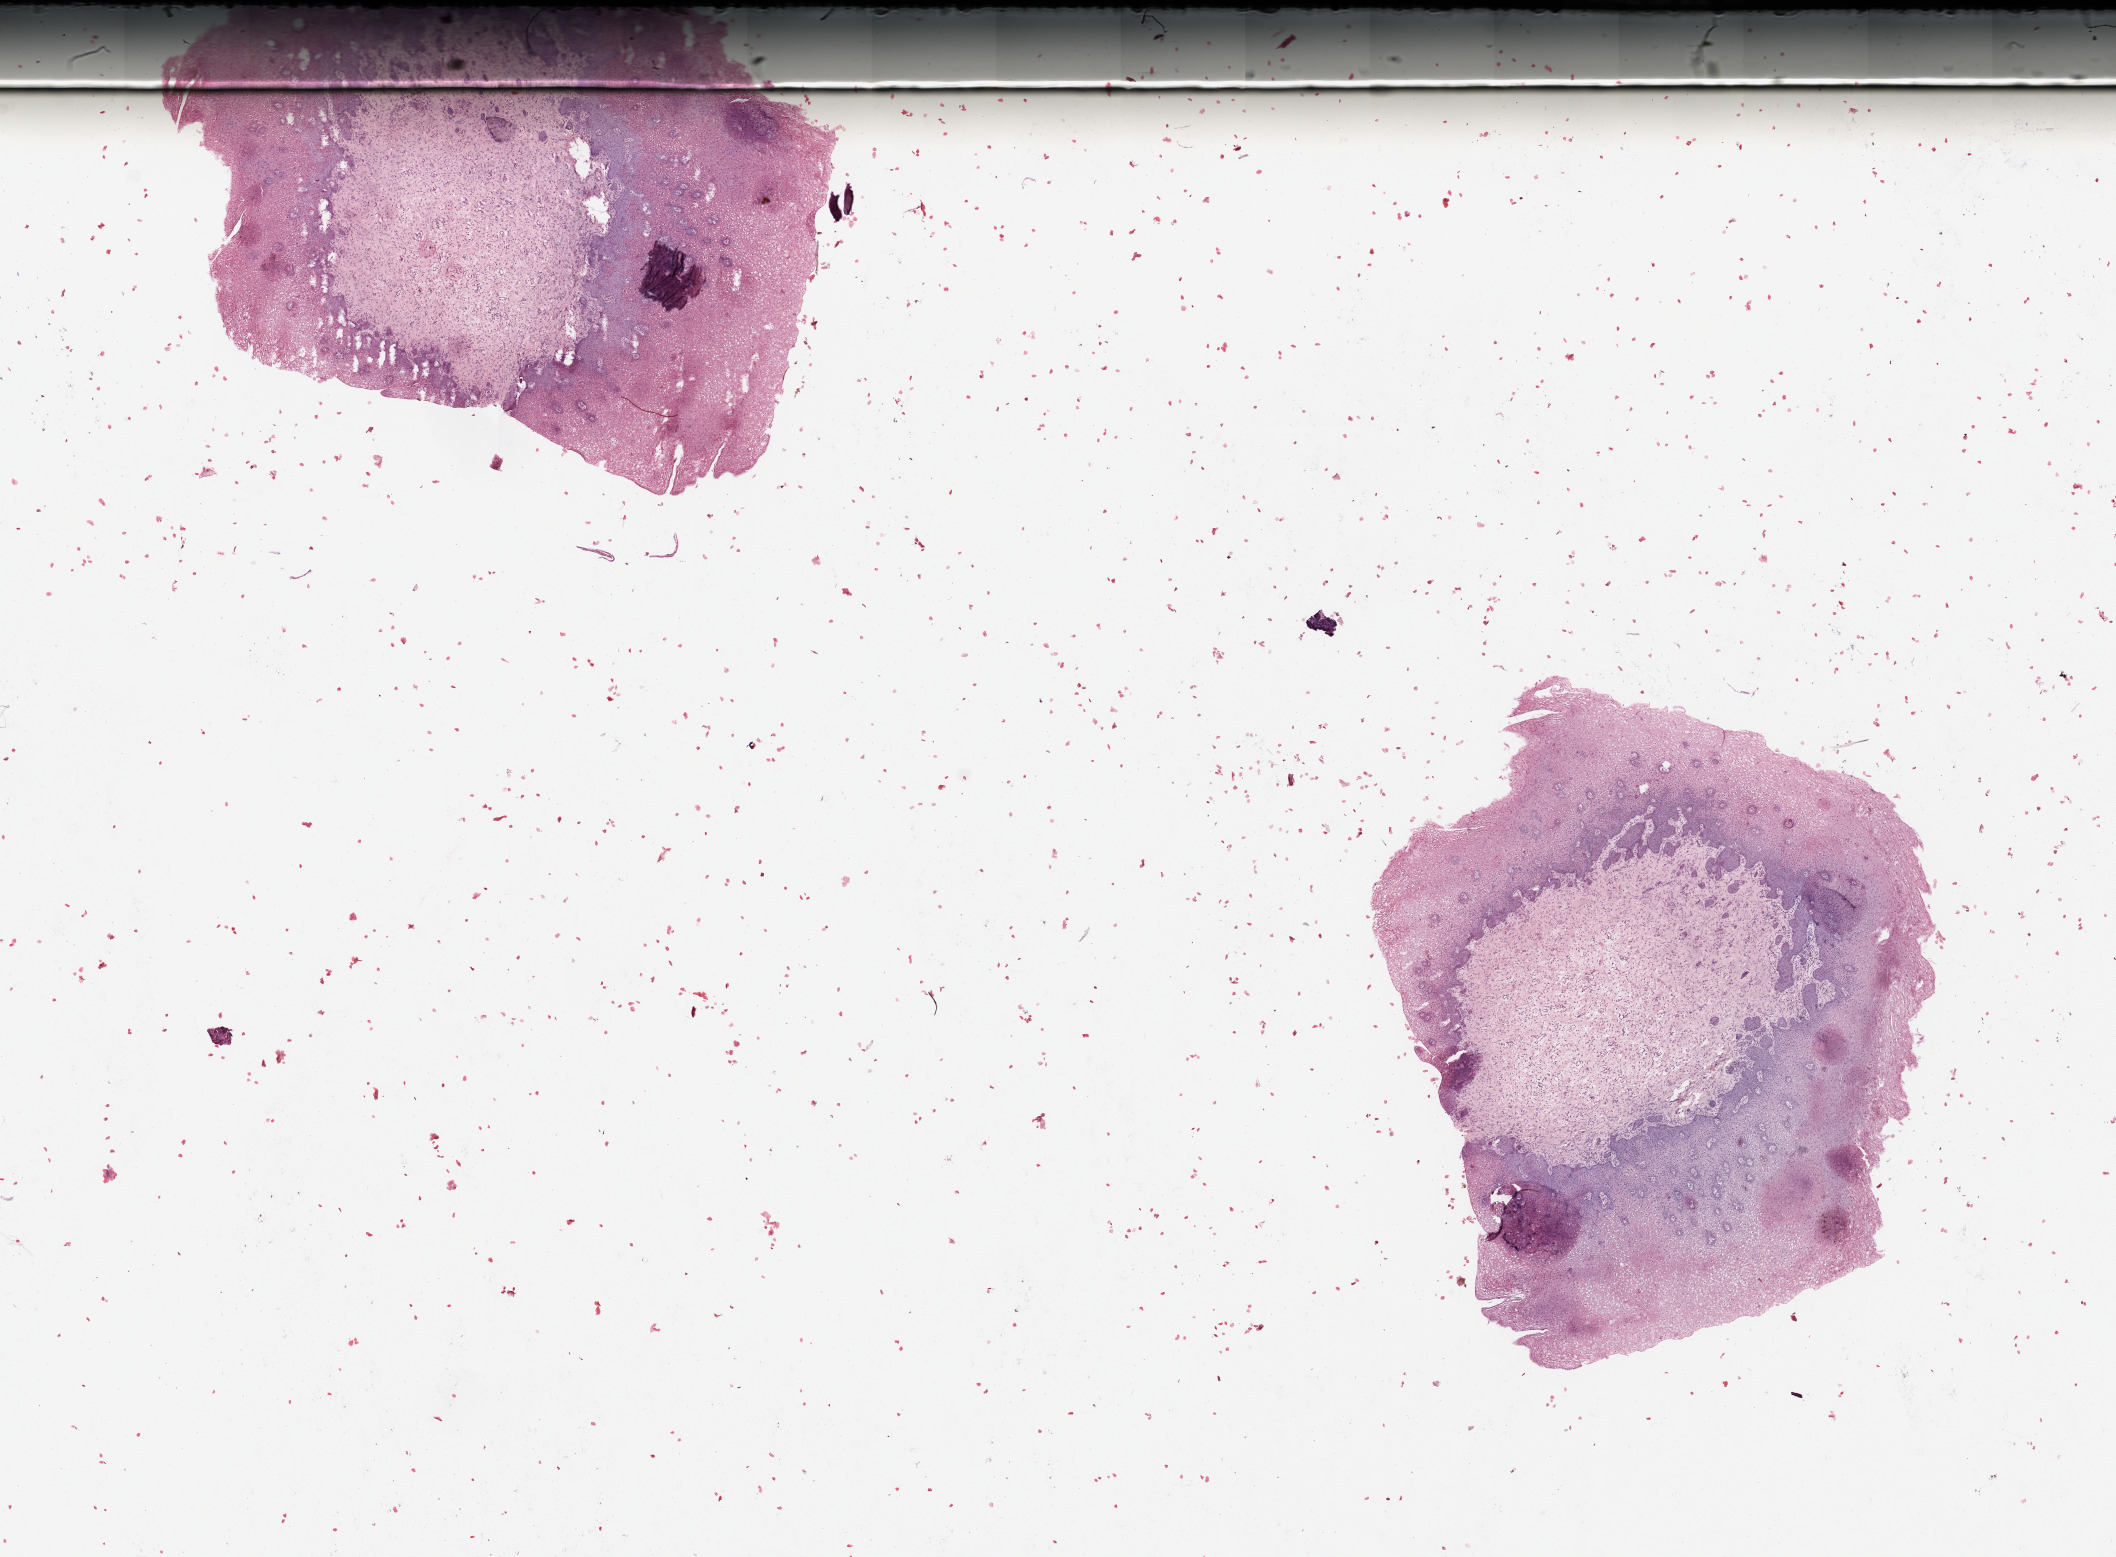
Digitized Hematoxylin and eosin (H&E) stained tissue section (whole slide), a low-resolution overview of the entire scanned area, about 16.7 x 12.3 mm (acquisition: 20x scan). Normal (non-tumour) tissue sample, uterus. Patient: female, age 41 years.
This section: normal (non-tumour) tissue from the same patient. Patient diagnosis: Endometrioid adenocarcinoma, NOS.